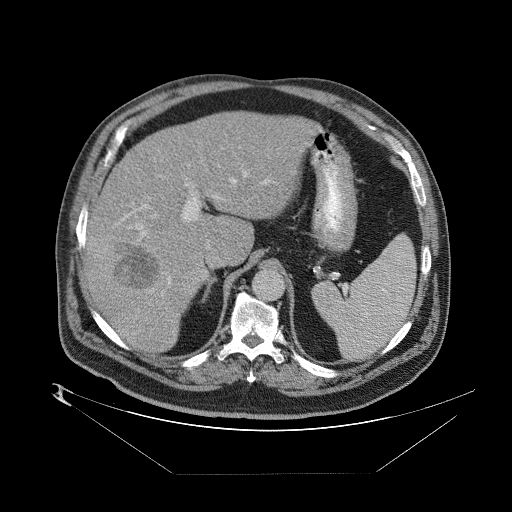
Contrast-enhanced abdominal CT (liver protocol), one axial slice; reconstruction kernel STANDARD; 140 kVp; one of 2 acquisitions stored at this slice position; soft-tissue window (W 400 / L 40 HU); 2.5 mm slice thickness; 512 × 512 image matrix. Case-level facts recorded for this patient, not image findings: diagnosis: hepatocellular carcinoma (patient treated with transarterial chemoembolisation; whether this scan precedes or follows treatment is not stated here); TNM stage (as recorded): Stage-II; Child-Pugh class: B; tumour differentiation: moderately differentiated; tumour size: 4 cm.
Outlined on this slice (semi-automatic segmentation, software-assisted and operator-edited):
- abdominal aorta: bounding box [x1, y1, x2, y2] px = [253, 268, 284, 299]
- liver parenchyma outside the tumour (the mass and vessels are separate outlines, so this box may not span the whole liver): [80, 108, 314, 352]
- mass: [113, 241, 211, 289]
- liver vessels: [87, 144, 241, 345]